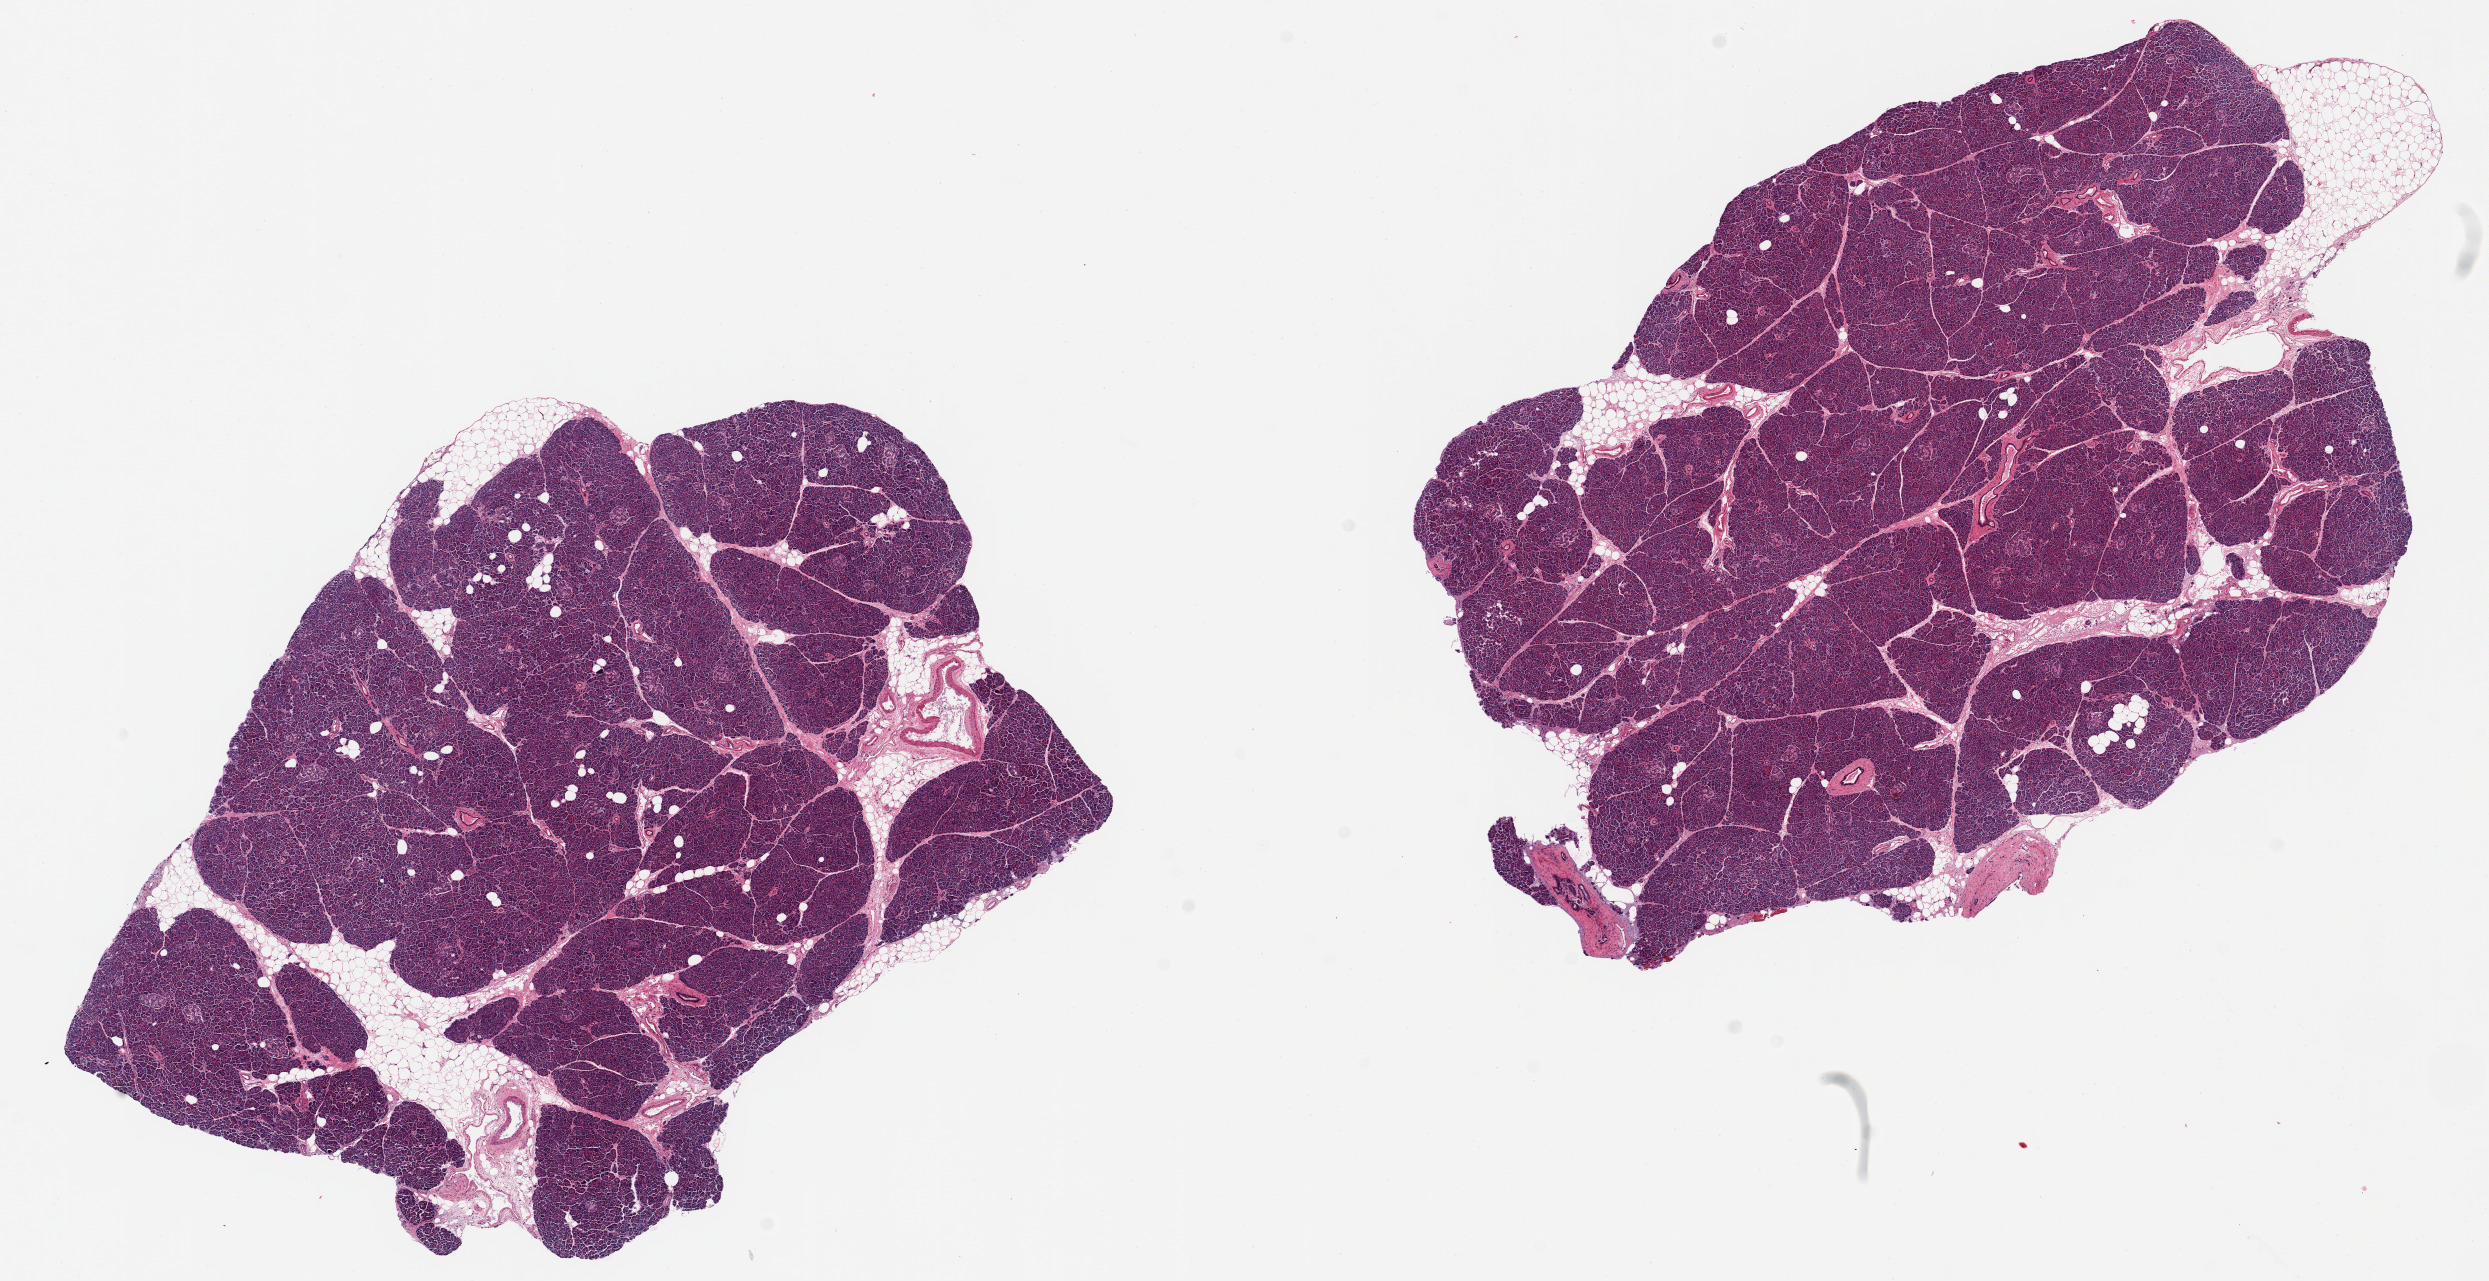
Digitized haematoxylin and eosin-stained section, brightfield — whole scanned area (about 19.7 x 10.1 mm) shown as a low-resolution overview. PAXgene-fixed paraffin-embedded (PFPE) section. Sampled site (target tissue): pancreas. Donor tissue sample. Donor: male.
- review note (as recorded): 2 pieces, 8x6 & 9x6mm; excellent preservation, one aliquot with ~1mm nubbin adherent fat; Islets well-seen